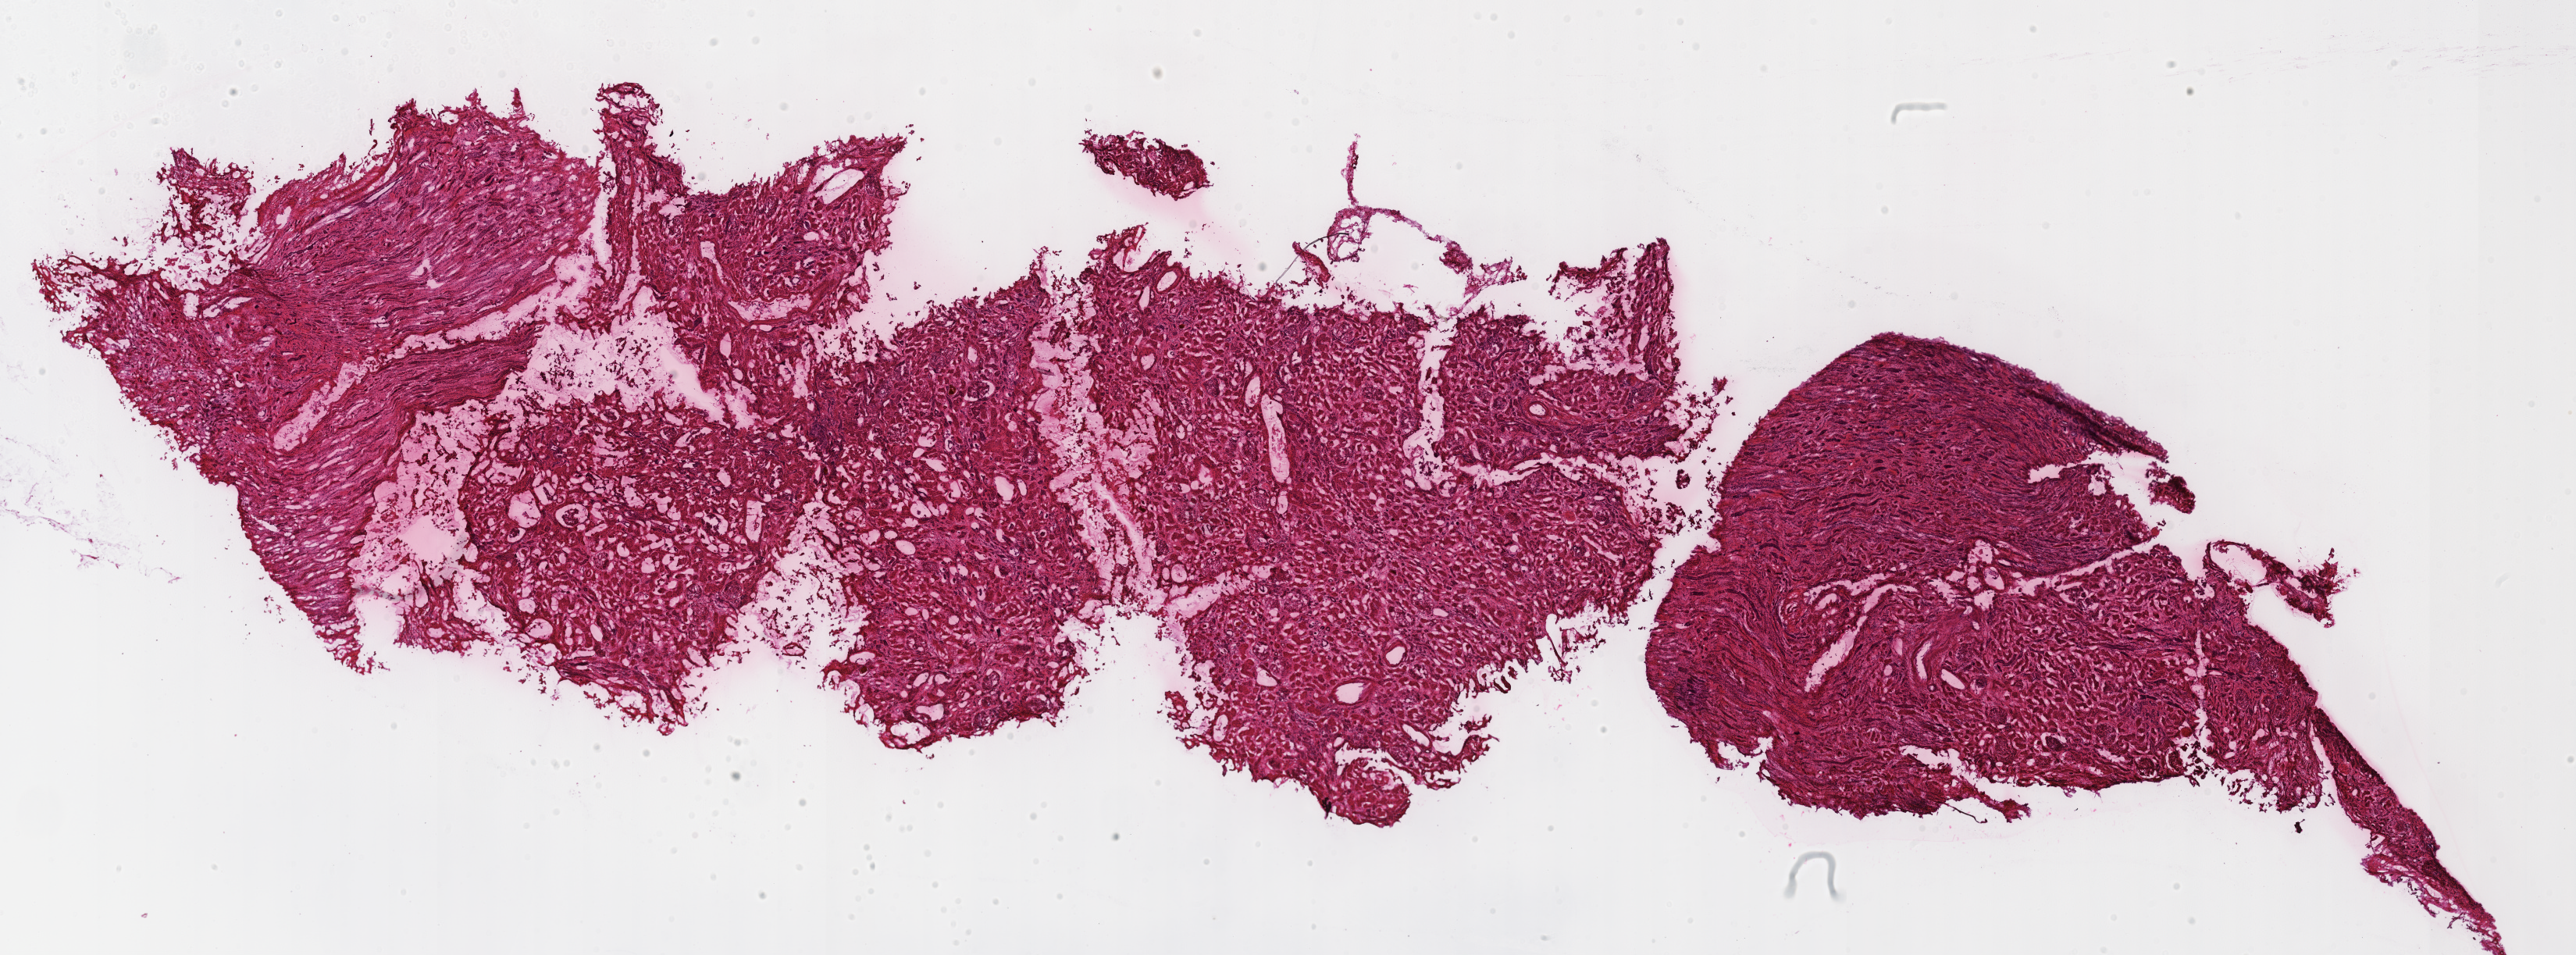
H&E-stained whole-slide image — whole scanned area (about 25.9 x 9.6 mm) shown as a low-resolution overview. Frozen section. Solid tissue normal (non-tumour tissue) sample from the kidney. Male, age 69 years at initial diagnosis.
* this section: solid tissue normal sample (biorepository sample class)
* patient diagnosis: Renal cell carcinoma, chromophobe type